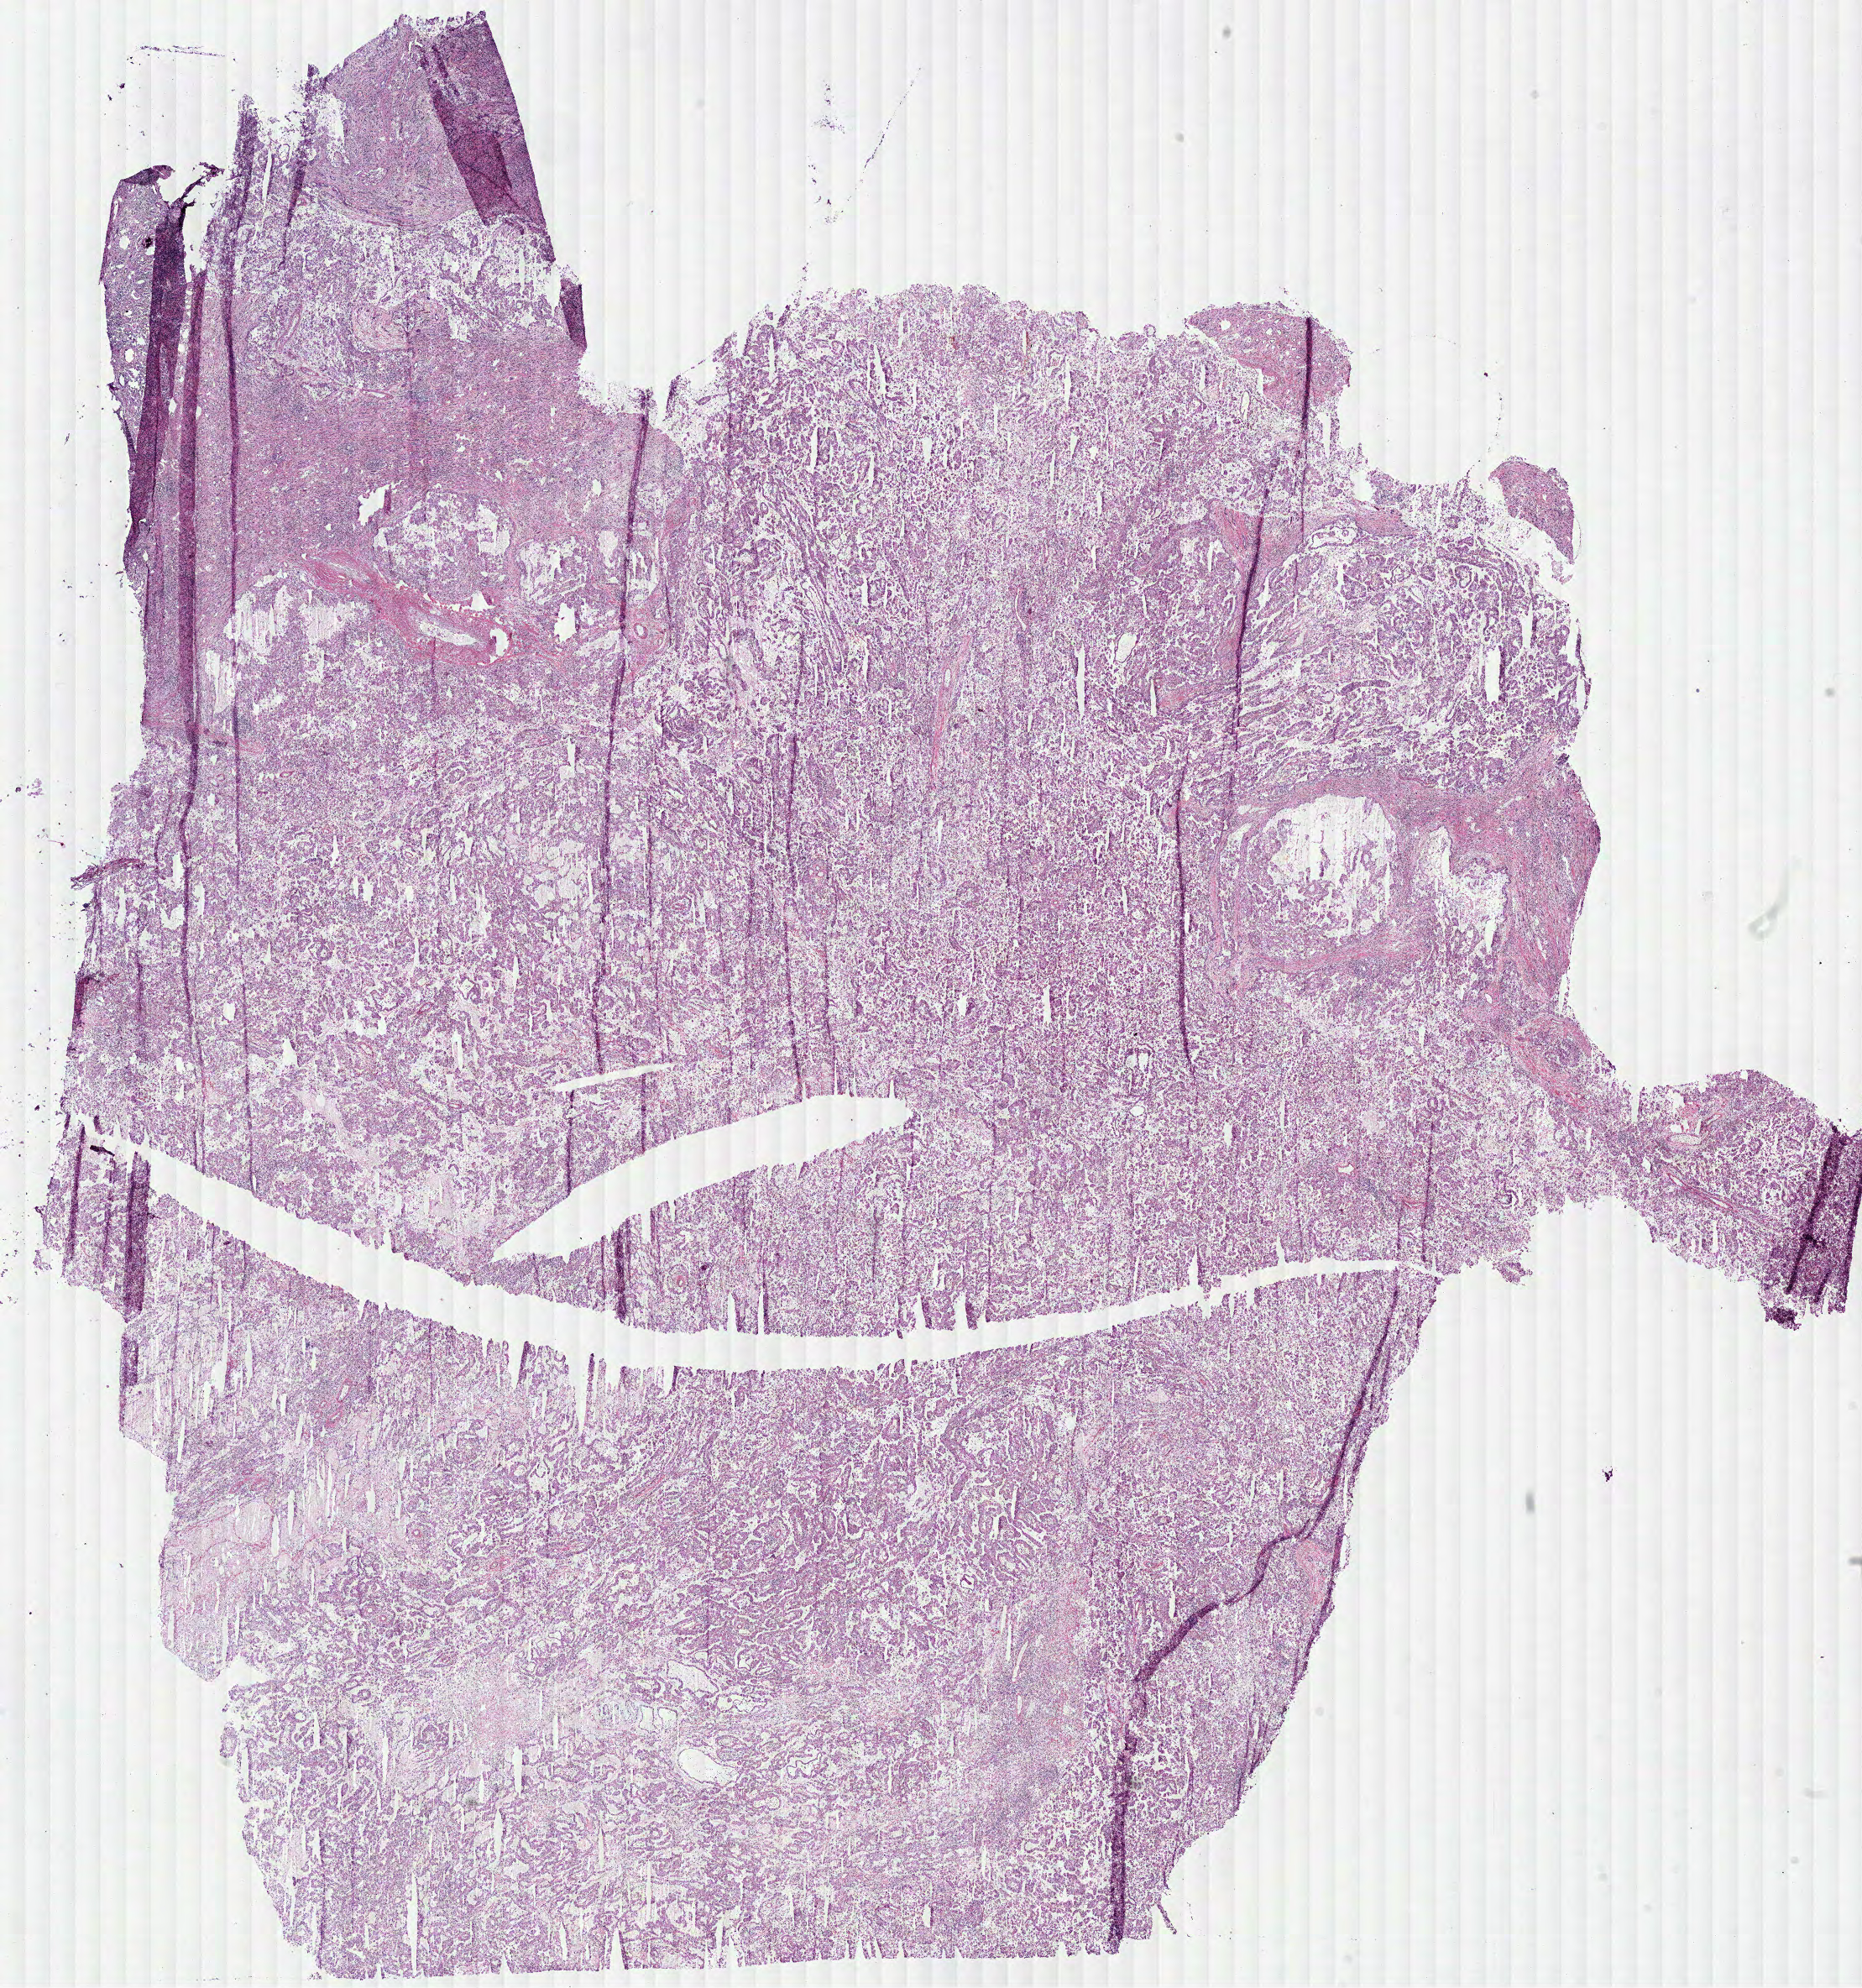
Whole-slide histology image, H&E-stained, a low-resolution overview of the entire scanned area, about 17.9 x 19.1 mm; frozen section from the bottom of the tissue portion; sample: primary tumour, kidney. Male, age 54 years at initial diagnosis. Slide review estimates, as recorded: tumour cells 82%, tumour nuclei 75%, normal cells 8%, stromal cells 10%, necrosis 0%.
AJCC pathologic stage: III. Histologic diagnosis: Papillary adenocarcinoma, NOS. Laterality: right. Lymph nodes positive (case pathology): 0 of 18 examined.